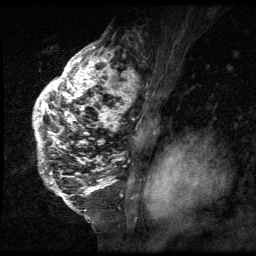
Breast MRI (dynamic contrast-enhanced), one sagittal slice; position 42 of 64 along the scan axis; 3 images stored at this slice position (order not interpretable as contrast timing); 1.5 T; TE 4.2 ms, TR 9 ms; 256 × 256 image matrix, field of view 180 × 180 mm. Patient: female, 50 years. Case-level facts recorded for this patient, not image findings: setting: breast cancer imaged before/during neoadjuvant chemotherapy; receptor status: triple-negative.
Structures marked on this image (semi-automatically segmented with operator editing):
- analysis volume of interest (the breast-tissue region the enhancement analysis was run in; not a lesion): box from (x=32, y=39) to (x=140, y=212) px
- tumour enhancement mask (voxels above the 140 % enhancement threshold inside the analysis volume of interest): (x=33, y=43)–(x=140, y=202)